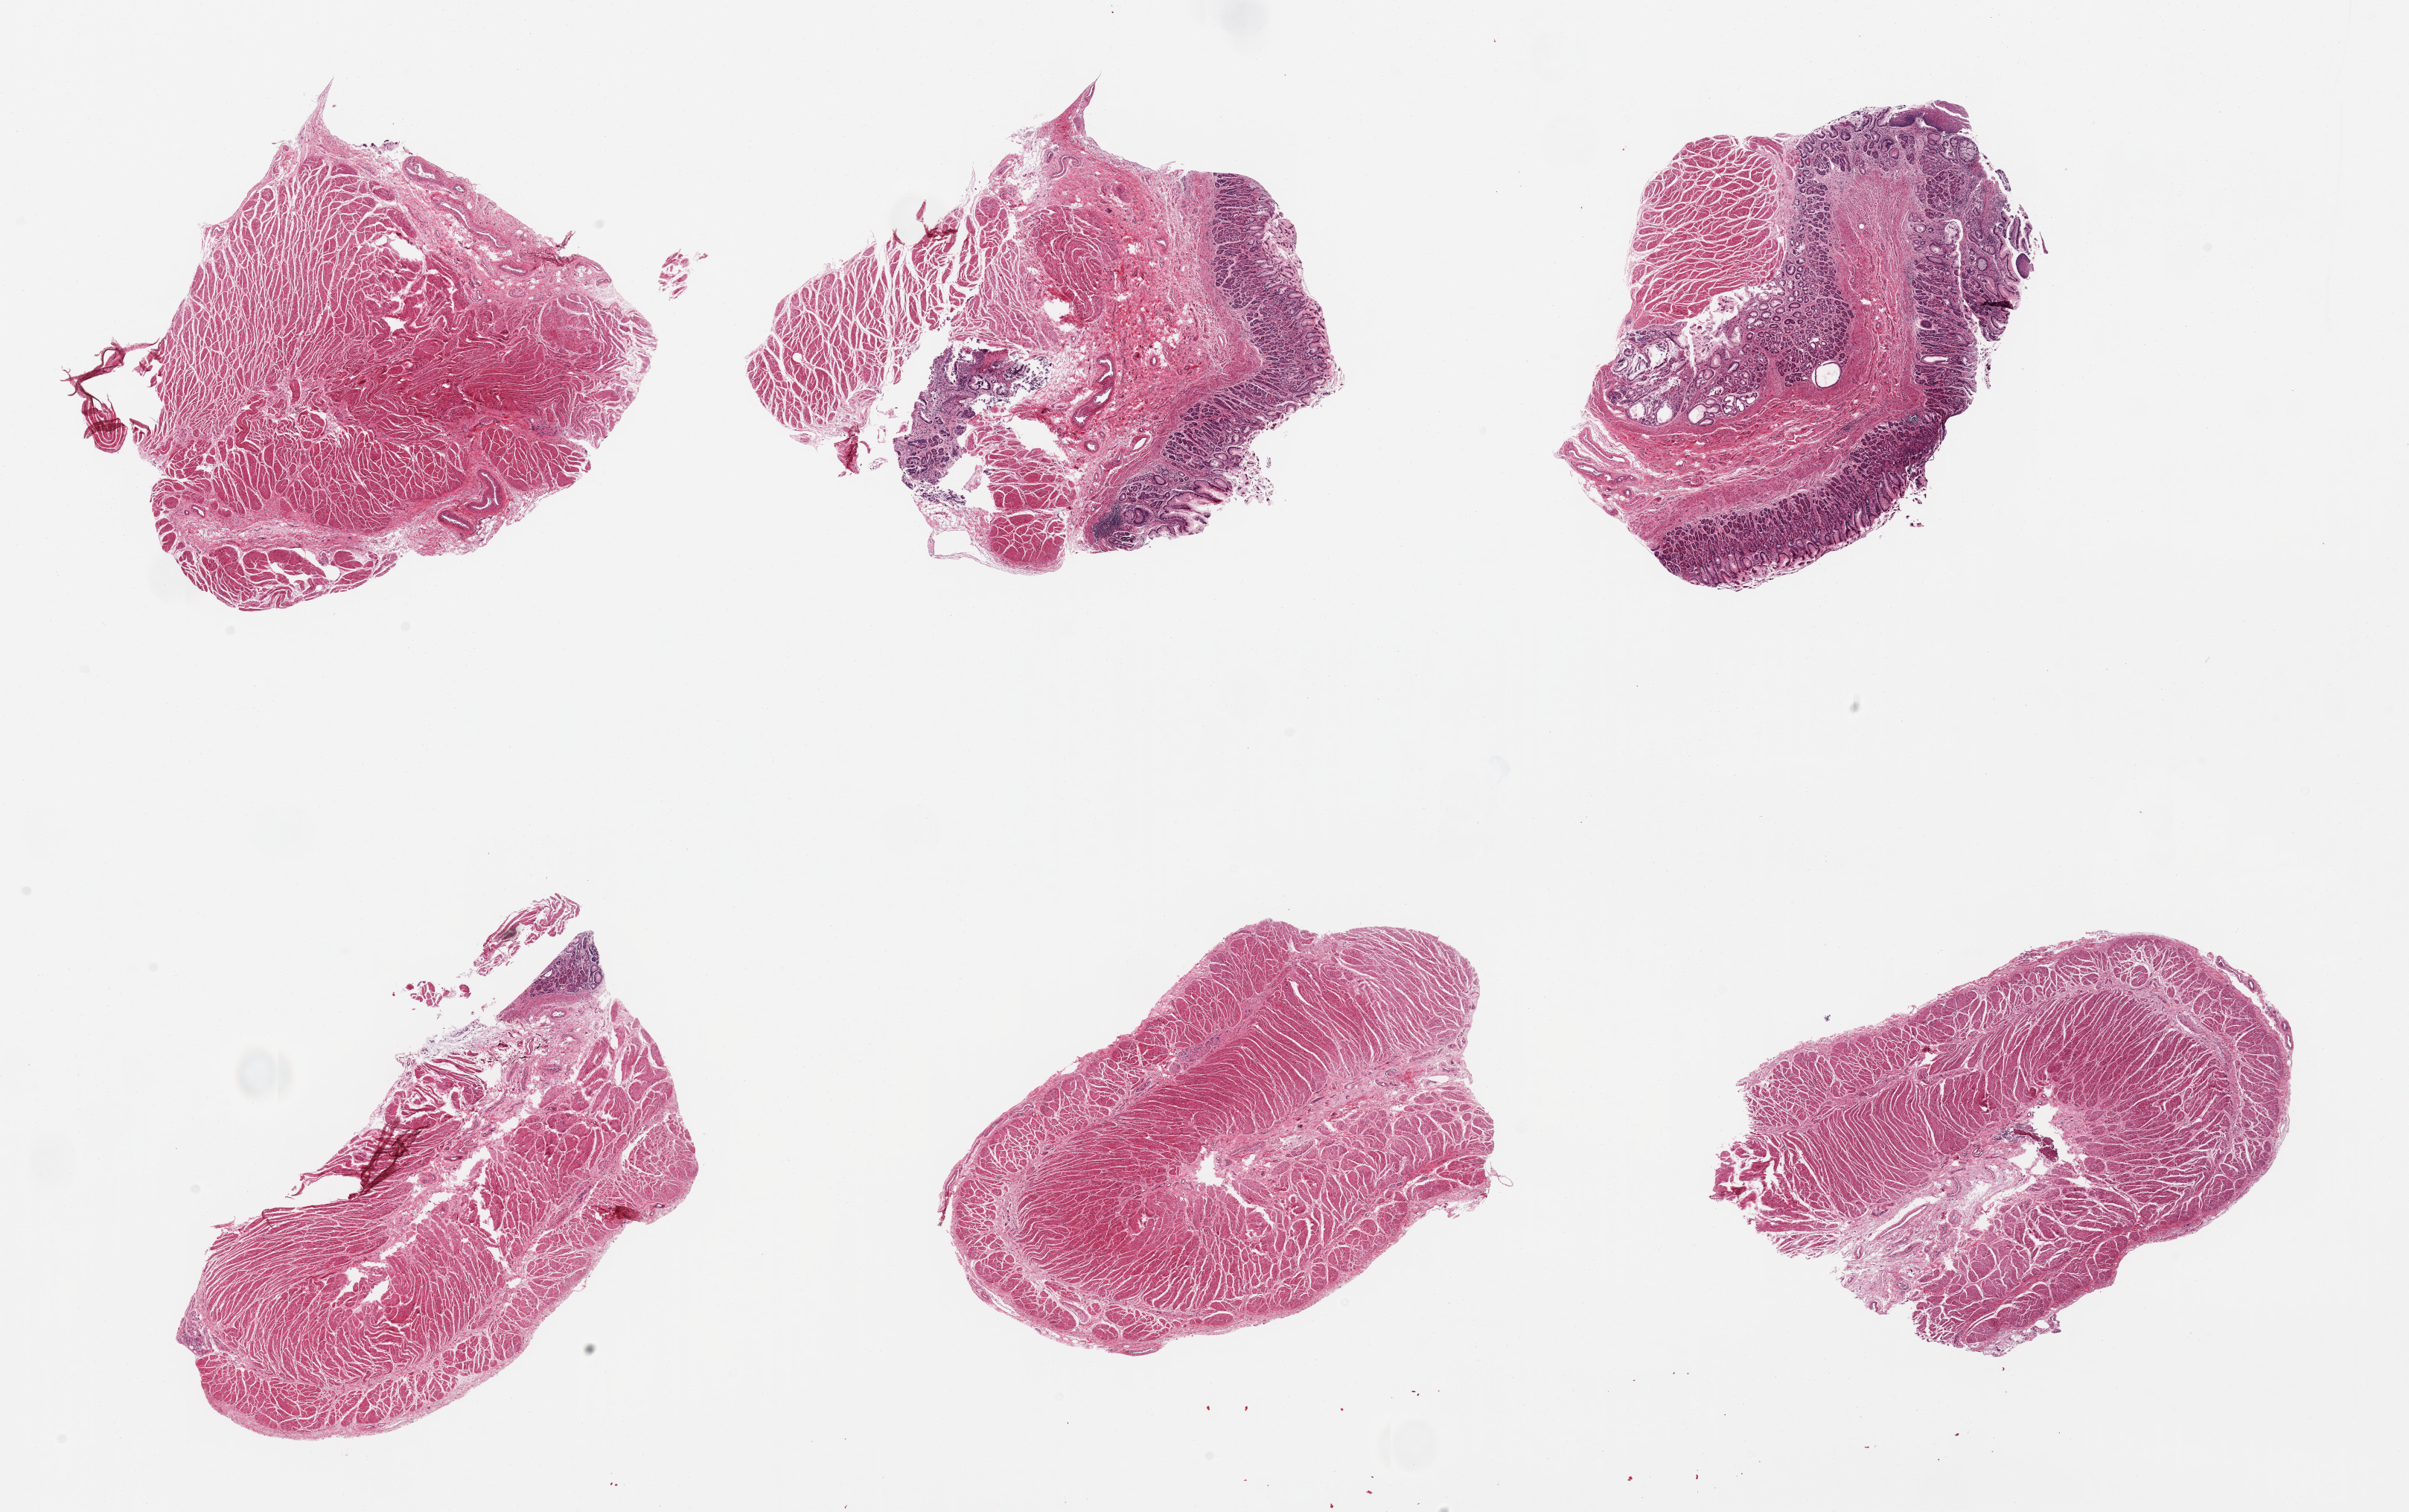
H&E whole-slide image — low-resolution overview of the scanned area, about 25.6 x 16.1 mm, PAXgene-fixed paraffin-embedded (PFPE) section, sampled site (target tissue): stomach, tissue donor sample. Donor sex: female.
Pathologist's review note for this sample: 6 pieces; predominantly muscularis with few pieces including mucosa (not gastric body).